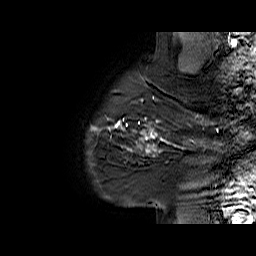
Breast MRI (dynamic contrast-enhanced), one sagittal slice. Position 55 of 60 along the scan axis. Dynamic contrast-enhanced series, time point 2 of 6 at this slice position (early post-contrast). 1.5 T. TE 6.1 ms, TR 32.9 ms. 4 mm slice thickness. 256 × 256 image matrix. Female patient. From the clinical record (not read from this slice): setting: breast cancer imaged before/during neoadjuvant chemotherapy; receptor status: HER2-positive.
Annotated regions visible in this slice (semi-automatic segmentation, software-assisted and operator-edited):
- analysis volume of interest (the breast-tissue region the enhancement analysis was run in; not a lesion): box from (x=127, y=95) to (x=194, y=165) px
- tumour enhancement mask (voxels above the 100 % enhancement threshold inside the analysis volume of interest): (x=127, y=96)–(x=193, y=151)